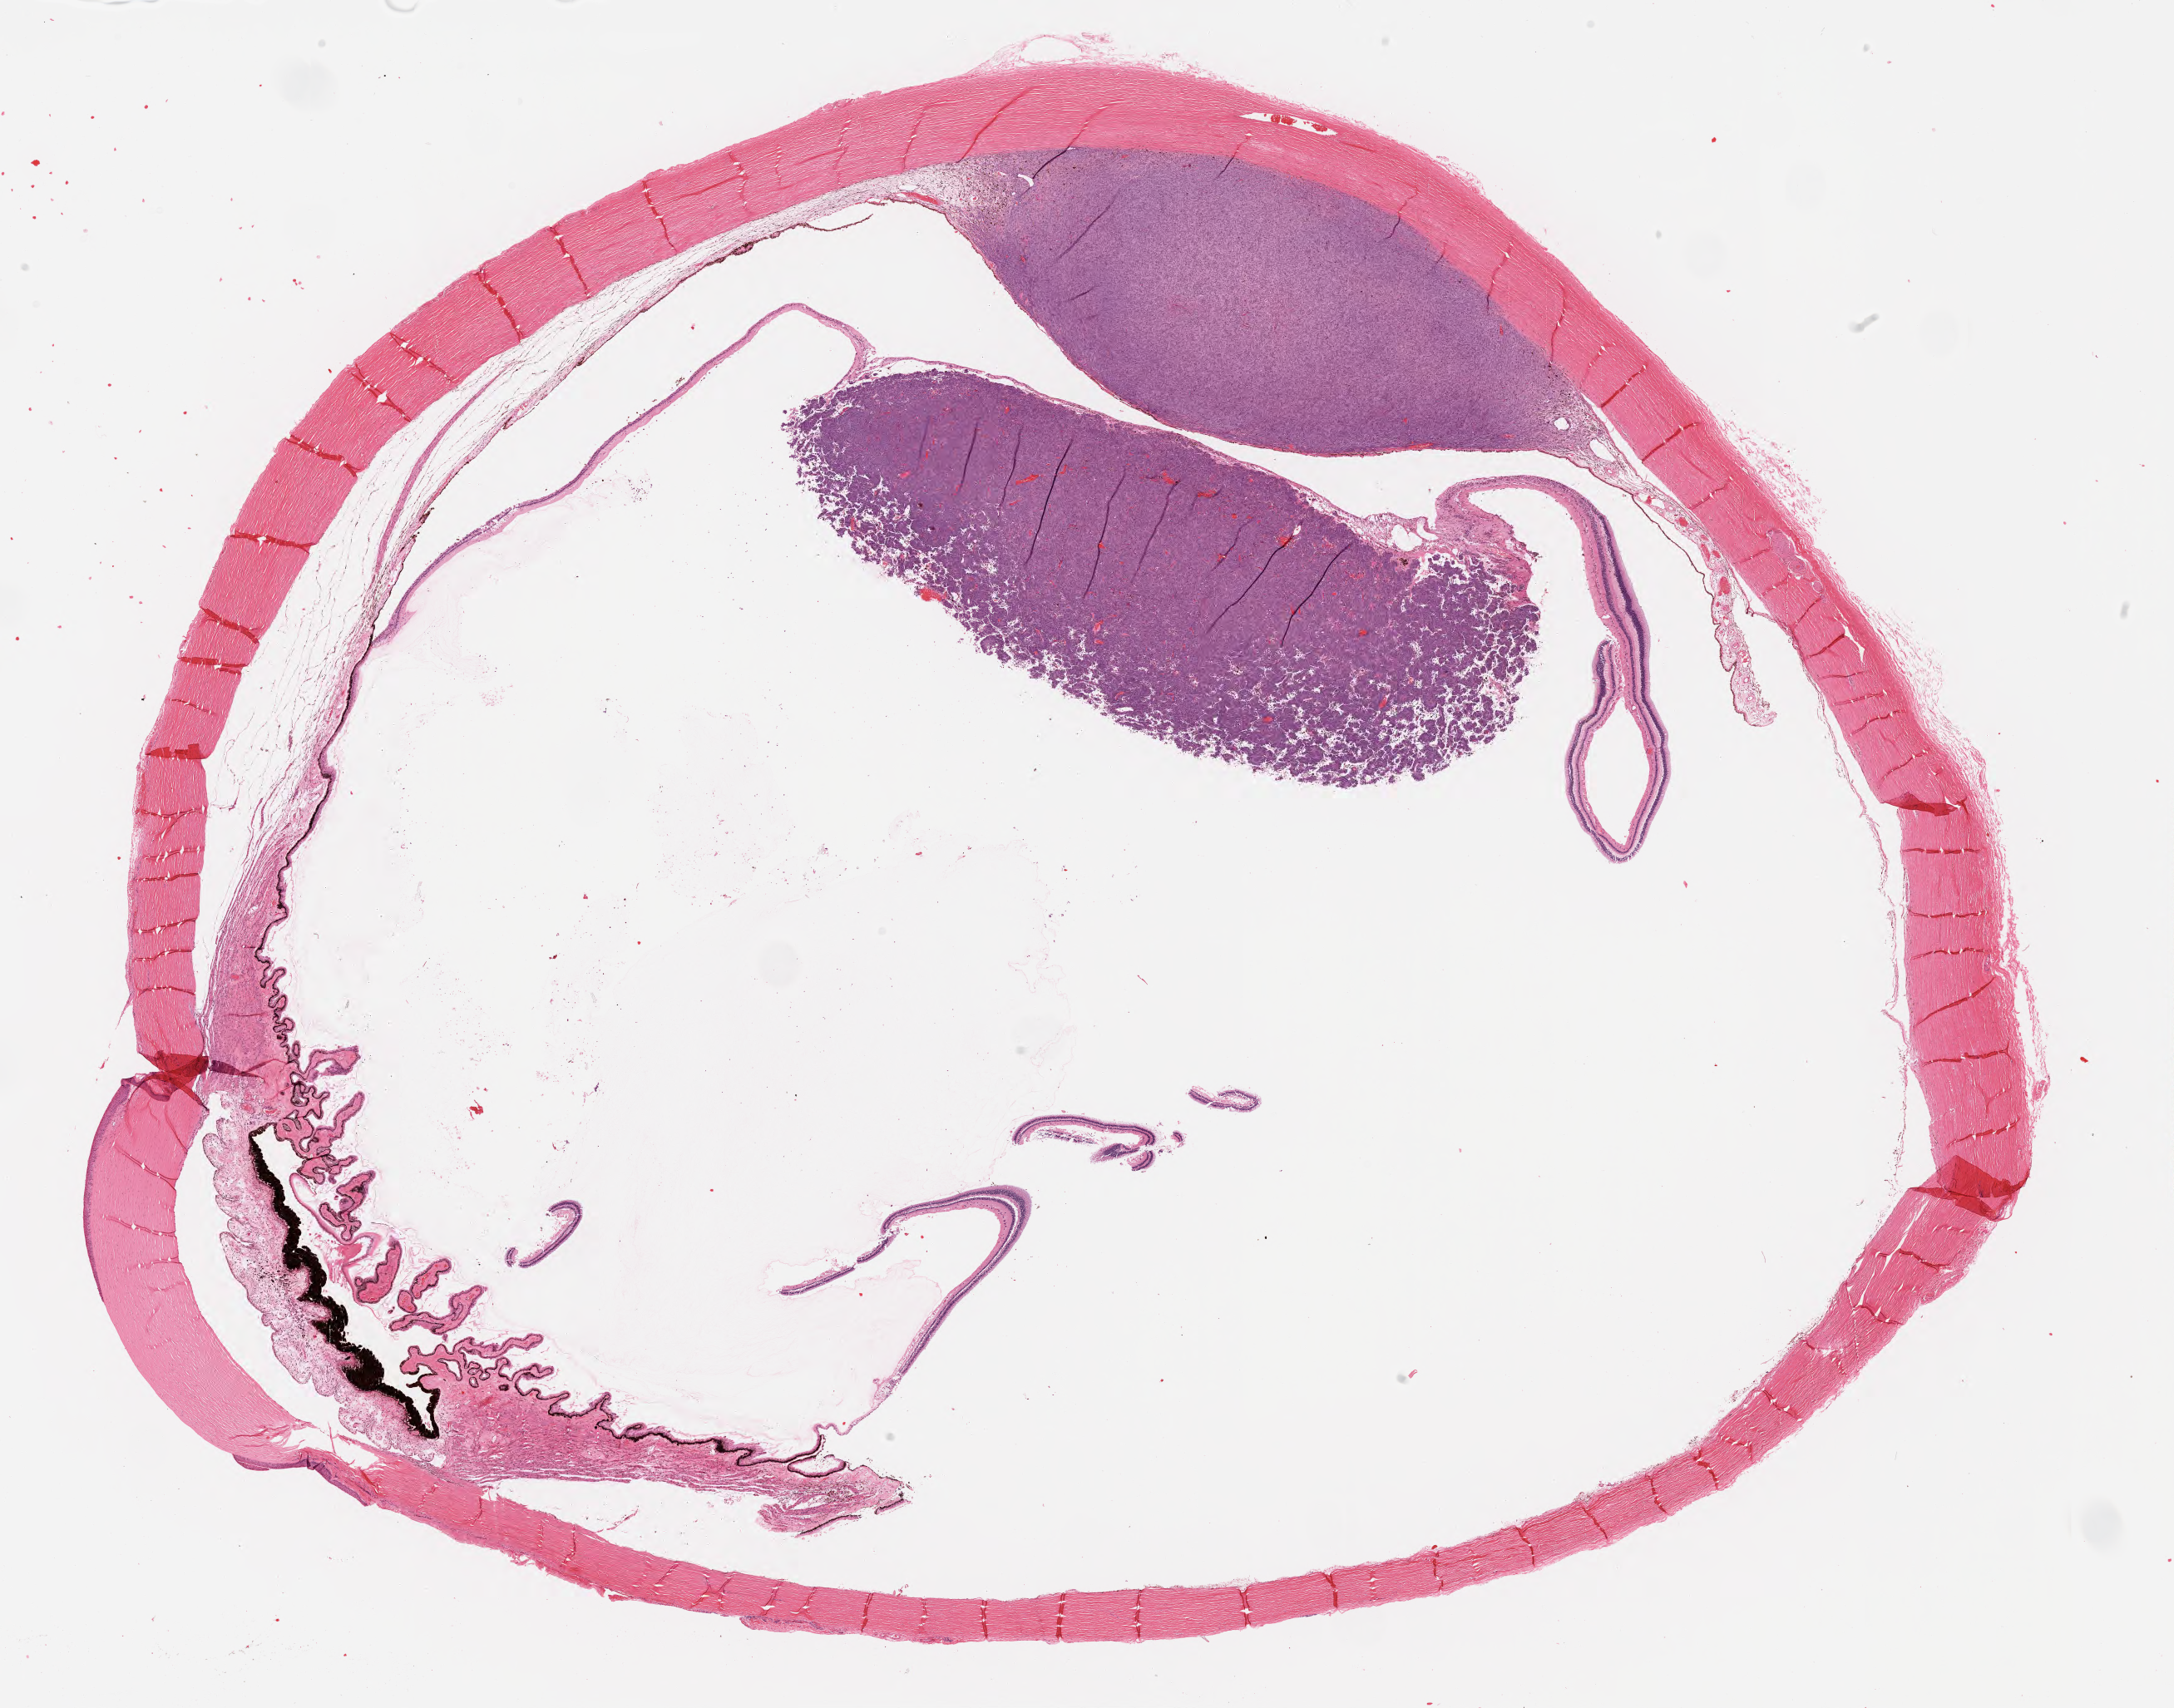
Hematoxylin and eosin (H&E) stained whole-slide image, shown as a low-resolution overview of the whole scanned area (about 20.6 x 16.2 mm, acquisition: 20x scan). Formalin-fixed paraffin-embedded (FFPE) diagnostic section. Primary tumour sample from the uvea. Patient: male, age at initial diagnosis 54 years.
• AJCC pathologic stage: IIB
• pathologic diagnosis: Epithelioid cell melanoma (choroid)